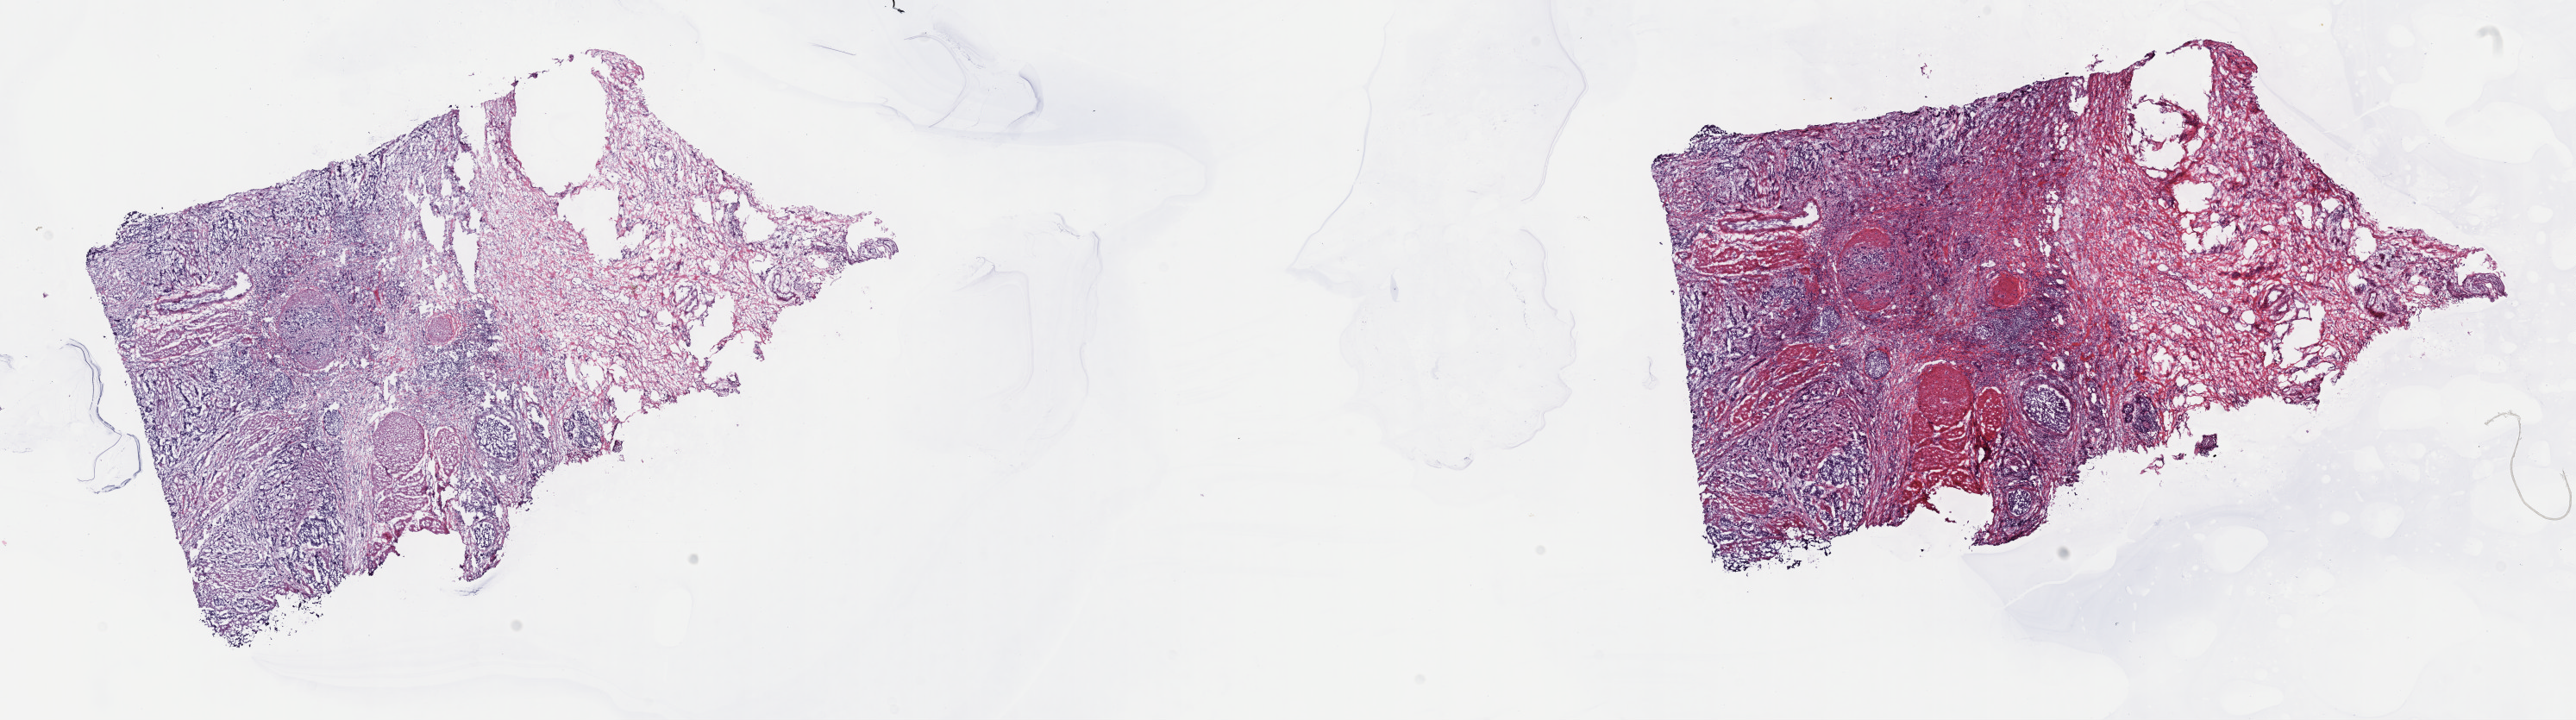
H&E whole-slide image, a low-resolution overview of the entire scanned area, about 24.2 x 6.8 mm; frozen section; sample: primary tumour, bladder. Patient: female, age at initial diagnosis 74 years. Histologic grade: high grade. Pathologist review of this section (percent, as recorded): tumour cells 70%, tumour nuclei 70%, normal cells 0%, stromal cells 30%, necrosis 0%. Inflammatory infiltration, as recorded: lymphocyte infiltration 2%, monocyte infiltration 1%, neutrophil infiltration 5%.
• histologic diagnosis: Papillary transitional cell carcinoma
• AJCC pathologic stage: IV (6th edition)
• lymph nodes positive (case pathology): 2 of 87 examined